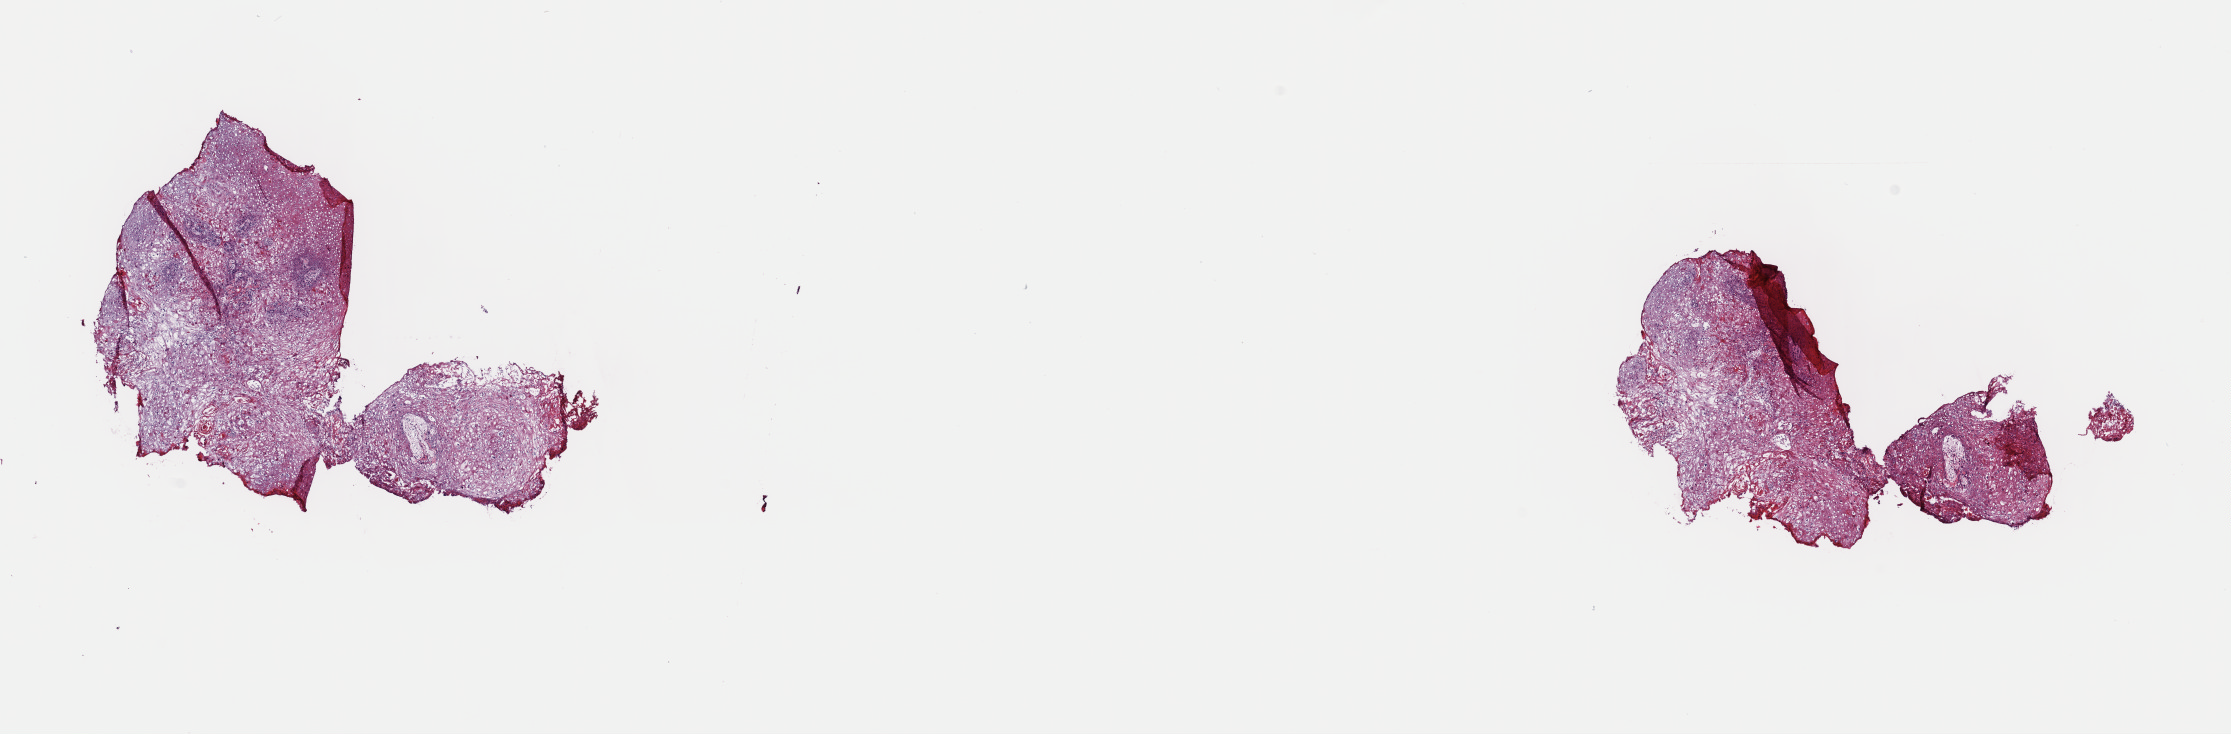
Digitized Hematoxylin and eosin (H&E) stained tissue section (whole slide), whole scanned area (about 17.6 x 5.8 mm, from a 40x scan) shown as a low-resolution overview. Frozen section. Primary tumour sample from the head and neck. Female patient; age at initial diagnosis 41 years. Histologic grade: G2 (moderately differentiated). Composition of this section per pathologist review: tumour cells 100%, tumour nuclei 80%, normal cells 0%, stromal cells 0%, necrosis 0%. Infiltration values recorded for this section: lymphocyte infiltration 3%, monocyte infiltration 0%, neutrophil infiltration 1%.
* histologic diagnosis: Squamous cell carcinoma, NOS (supraglottis)
* TNM: T4a N2c M0
* AJCC pathologic stage: IVA (7th edition)